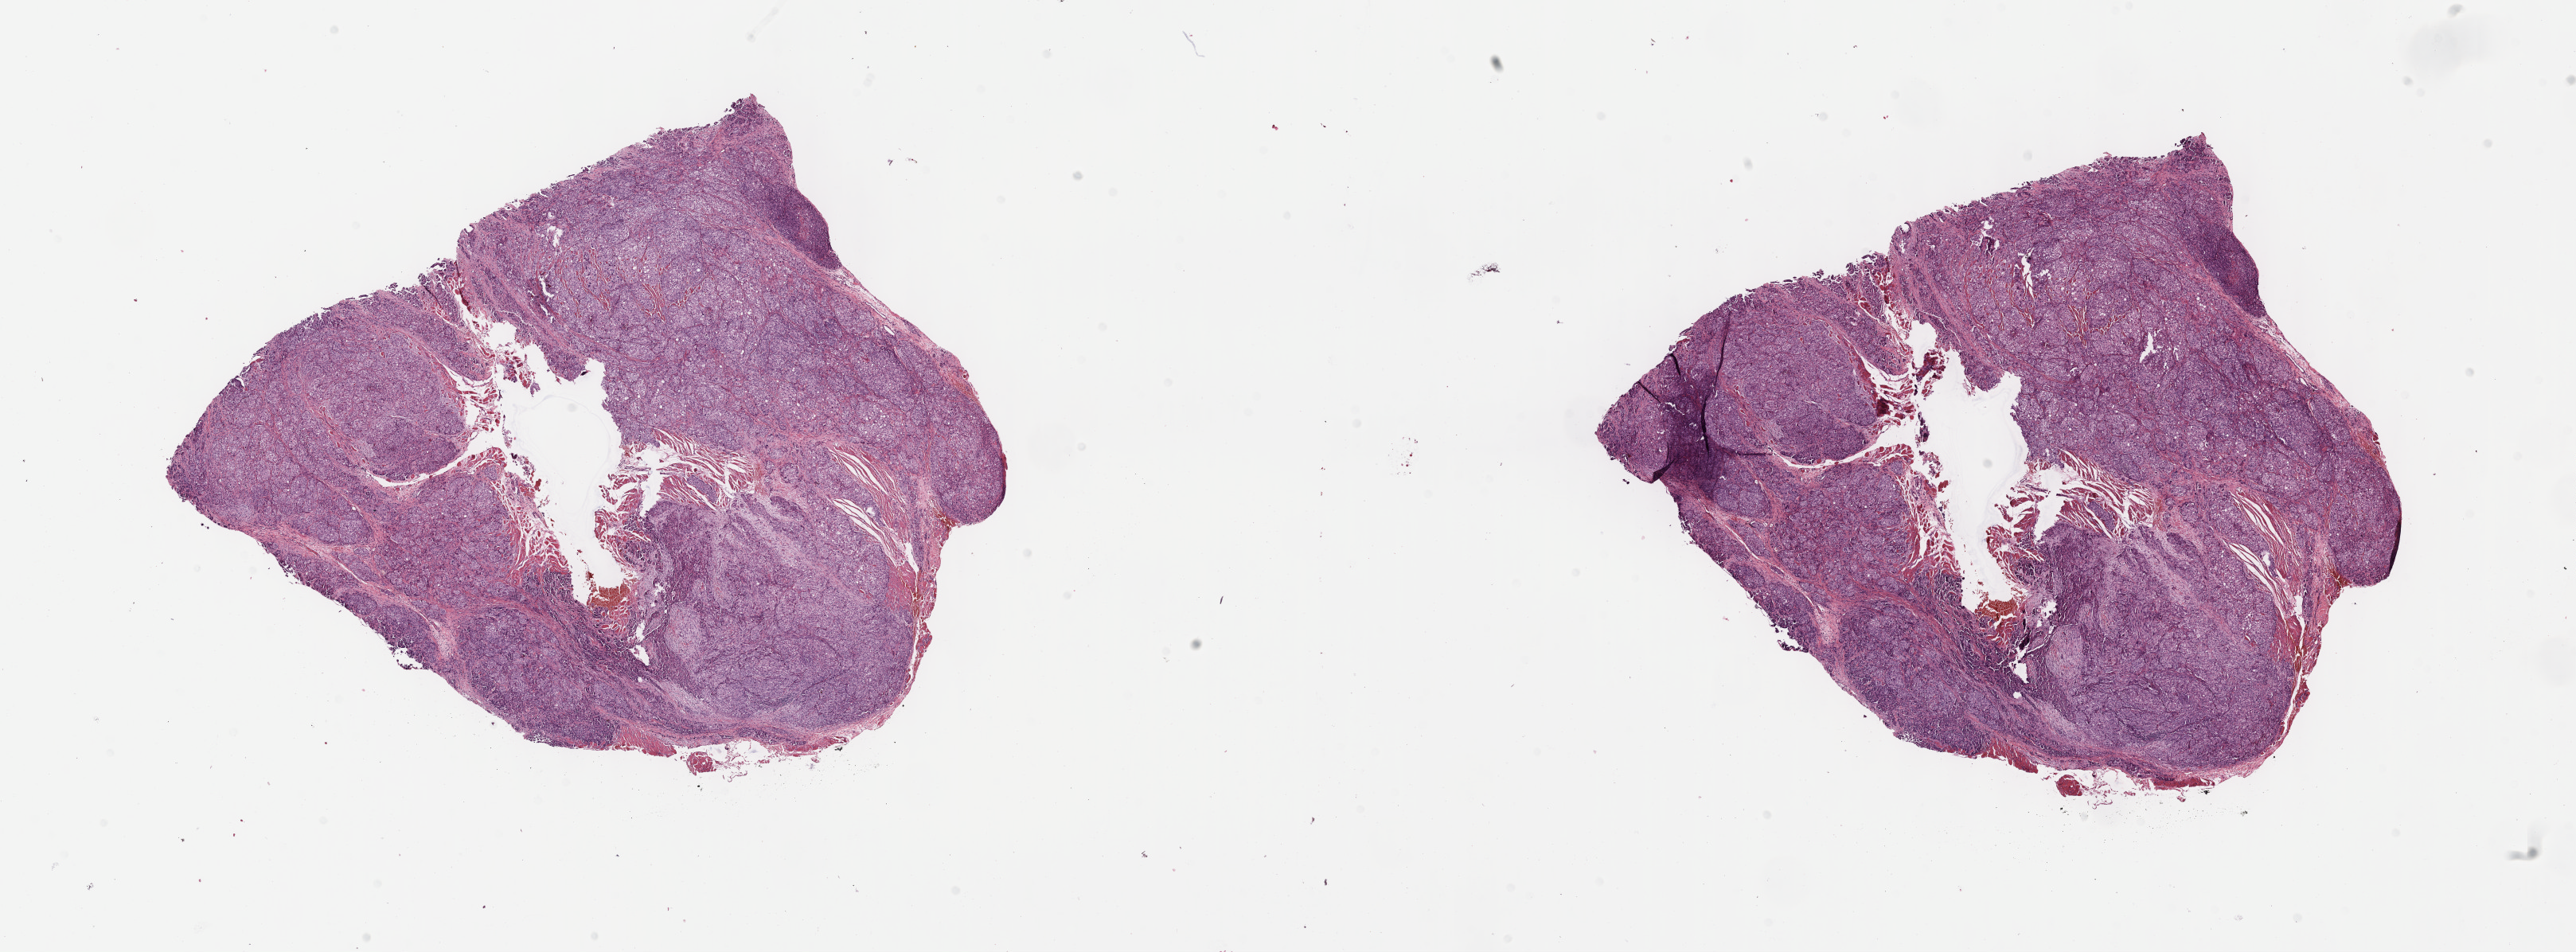
Whole-slide histology image, H&E-stained, low-resolution overview of the scanned area, about 26.2 x 9.7 mm (from a 40x scan), FFPE section, sample: primary tumour, mesothelium. Female patient; age at initial diagnosis 28 years.
Pathologic diagnosis: Epithelioid mesothelioma, malignant (pleura, NOS). AJCC pathologic stage: IV (6th edition).